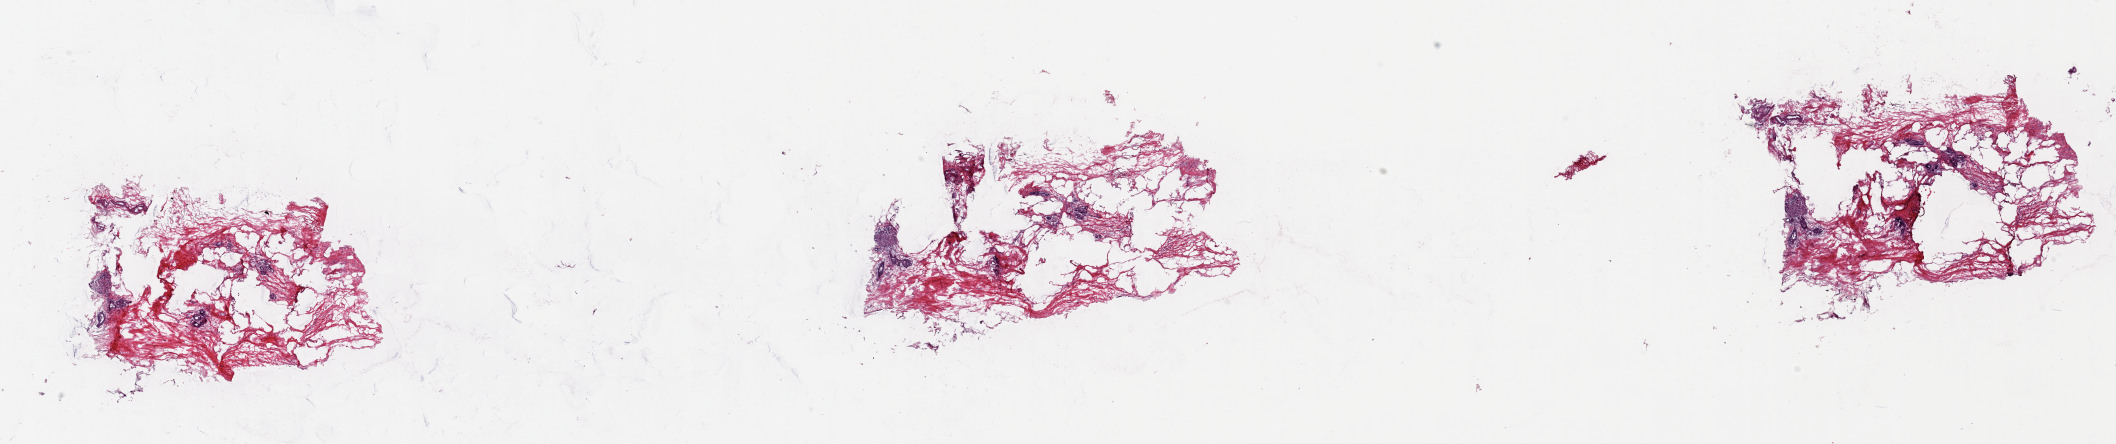
Hematoxylin and eosin (H&E) stained whole-slide image — low-resolution overview of the scanned area, about 33.4 x 7.0 mm. Frozen section from the top of the tissue portion. Solid tissue normal (non-tumour tissue) sample from the breast. Patient: female, age at initial diagnosis 87 years. Composition of this section per pathologist review: tumour cells 0%, tumour nuclei 0%, normal cells 10%, stromal cells 90%, necrosis 0%. Infiltration values recorded for this section: lymphocyte infiltration 0%, monocyte infiltration 0%, neutrophil infiltration 0%.
* this section: solid tissue normal (non-tumour) sample from the same patient
* patient diagnosis: Lobular carcinoma, NOS